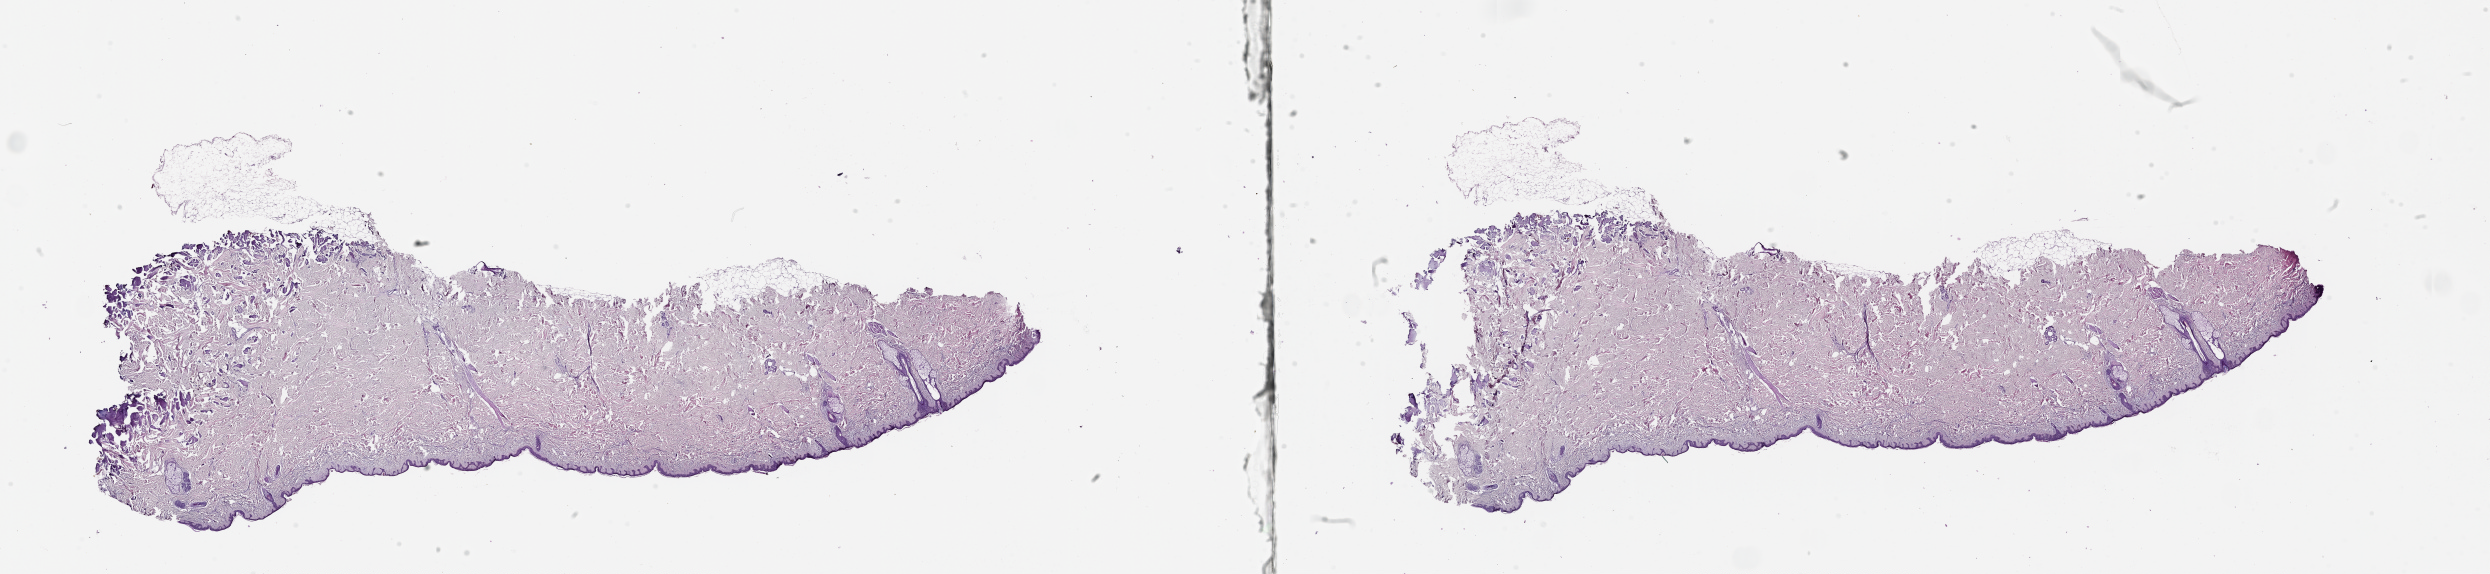
H&E whole-slide image — low-resolution overview of the scanned area, about 40.1 x 9.2 mm (slide scanned at 20x), normal (non-tumour) tissue sample, sampled site: trunk. 81-year-old female patient.
* this section: normal (non-tumour) tissue from the same patient
* patient diagnosis: Malignant melanoma, NOS